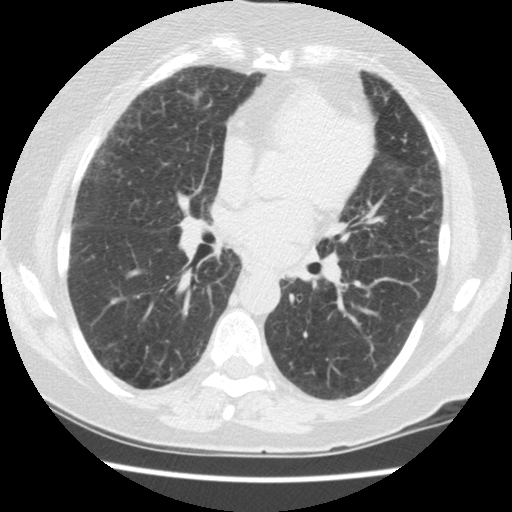
Chest CT (low-dose screening protocol), one axial image, second annual screen, lung window (W 1500 / L -600 HU), 2.5 mm slice thickness, standard (soft-tissue) reconstruction kernel (STANDARD), slice 68 of 134 in the series. Female participant, aged 60 years at enrolment. Former smoker at enrolment.
Expert reader's lesion annotation, box from (x=271, y=252) to (x=318, y=298) px. The exam's reader record, not a measurement of the box and not confirmed to be the same lesion: non-calcified nodule or mass ≥4 mm, left lower lobe, 5 × 4 mm, smooth margins, soft tissue attenuation, pre-existing on the prior screen: yes; interval growth: no. Lung cancer was diagnosed 423 days after this screen (after the third annual screen): small cell carcinoma, NOS, left lower lobe, undifferentiated (G4), stage IV (AJCC 6th edition), 69 mm at pathology.